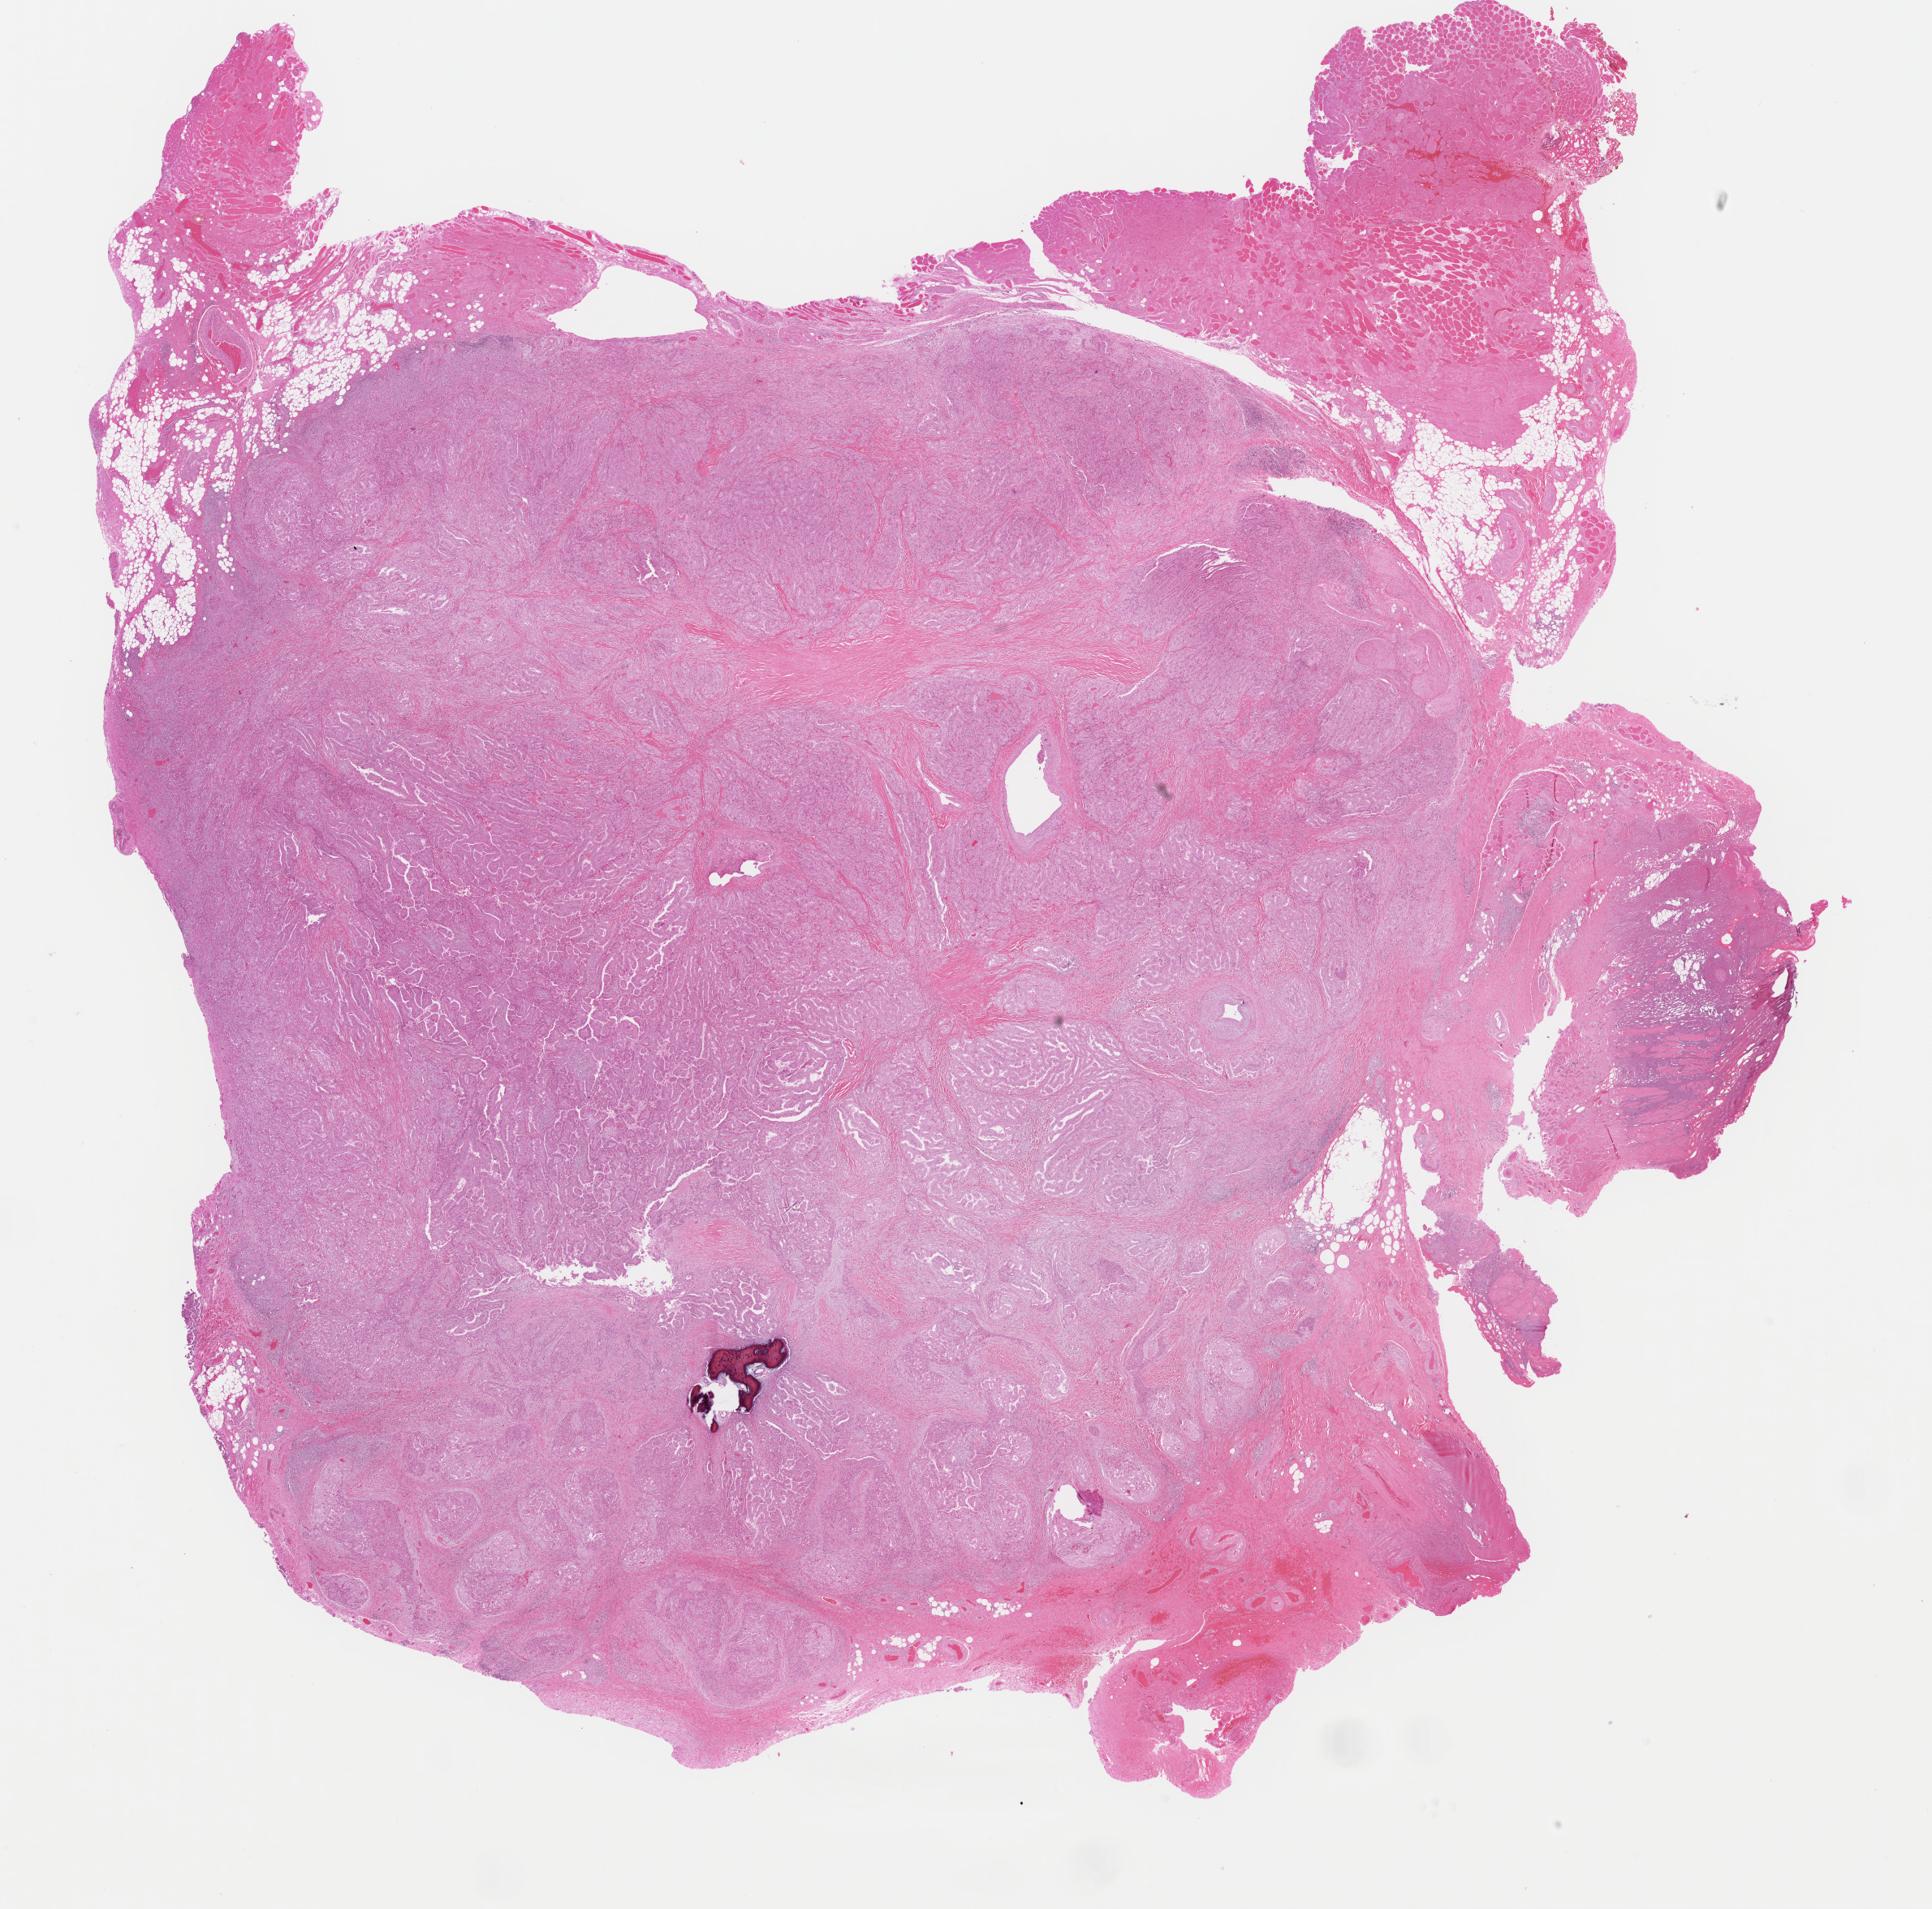
Whole-slide histology image, Hematoxylin and eosin (H&E) stained — whole scanned area (about 18.8 x 18.6 mm, acquisition: 40x scan) shown as a low-resolution overview, formalin-fixed paraffin-embedded (FFPE) diagnostic section, thyroid, primary tumour sample. Female patient; age at initial diagnosis 79 years.
• lymph nodes positive (case pathology): 1 of 7 examined
• pathologic diagnosis: Papillary adenocarcinoma, NOS (thyroid gland)
• laterality: right
• TNM: T3 N1 M0
• AJCC pathologic stage: III (6th edition)